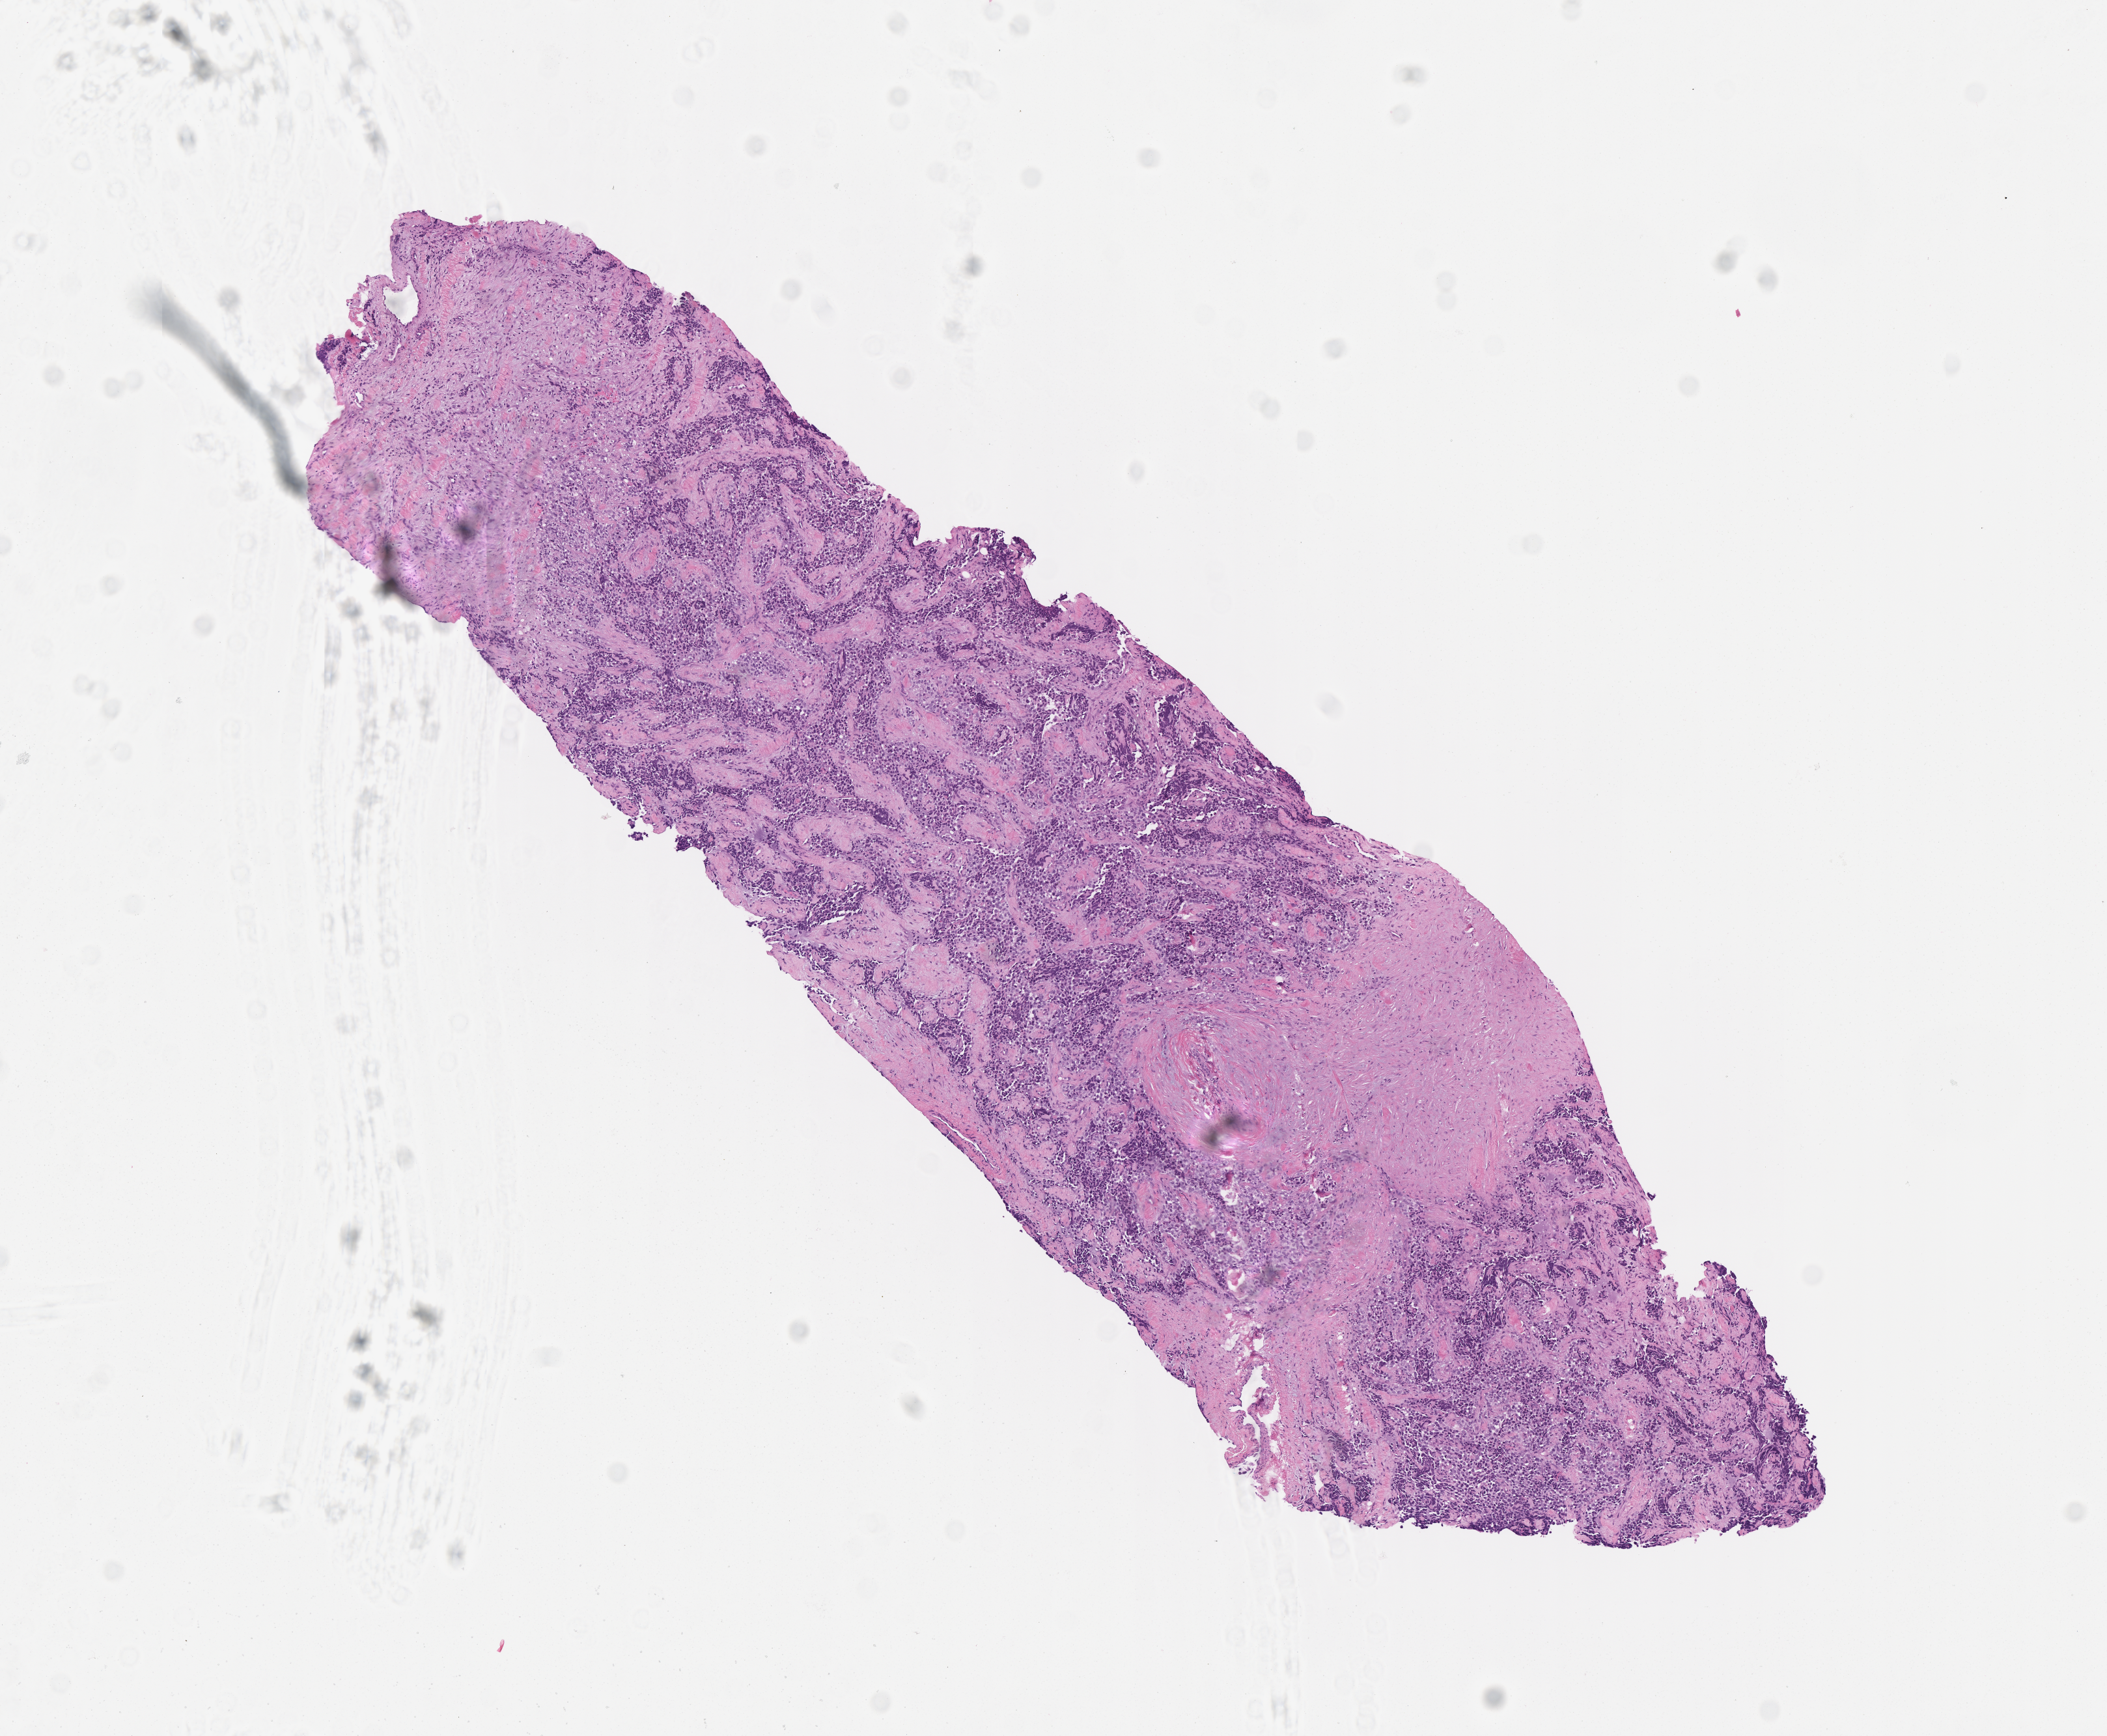
Digitized hematoxylin and eosin (H&E)-stained section of tumor tissue — shown as a low-resolution overview of the whole scanned area (about 6.5 x 5.4 mm); formalin-fixed paraffin-embedded section; site: soft tissue, chest-left. Patient: male, age 8.8 years at diagnosis.
- metastatic status at presentation (as recorded): metastatic (confirmed)
- diagnosis: rhabdomyosarcoma; histological classification: alveolar rhabdomyosarcoma
- stage (as recorded): 4